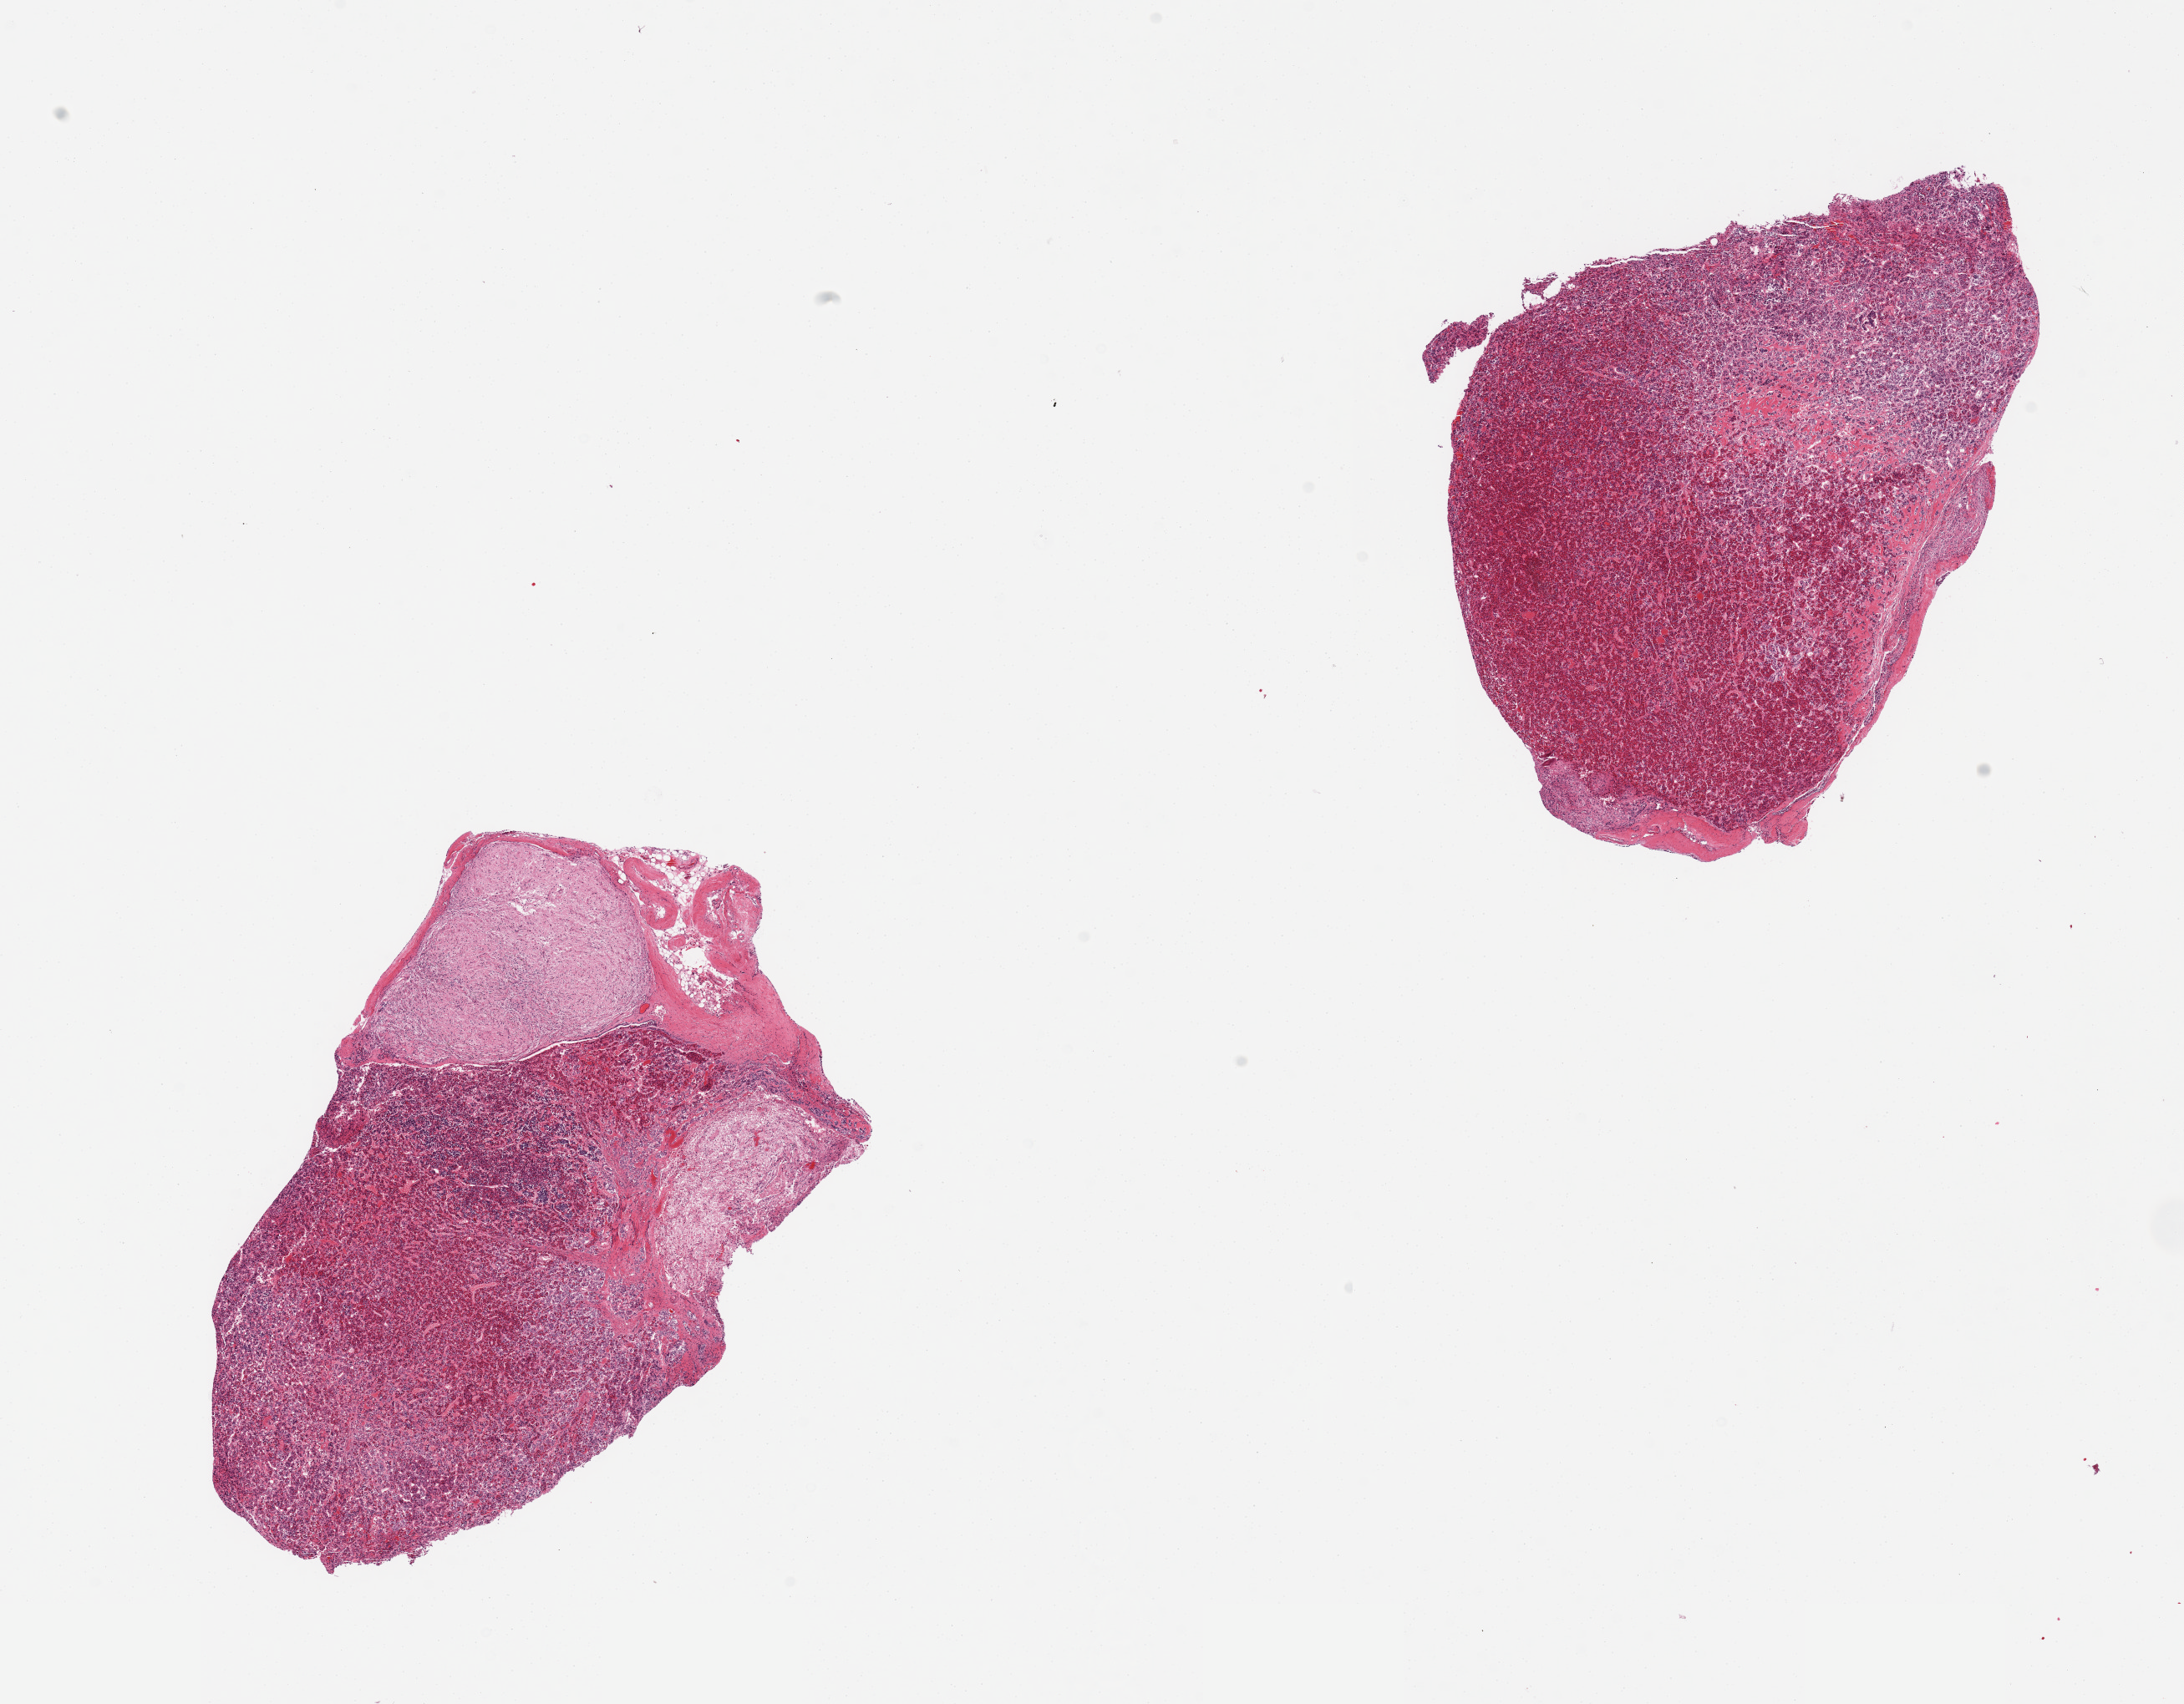
Digitized haematoxylin and eosin-stained section, brightfield — low-resolution overview of the scanned area, about 20.7 x 16.1 mm (from a 20x scan), PAXgene-fixed paraffin-embedded (PFPE) section, section of pituitary (target tissue), donor tissue sample. Male donor.
Pathologist's review note for this sample: 2 pieces, adenohypophysis and neurohypophysis.